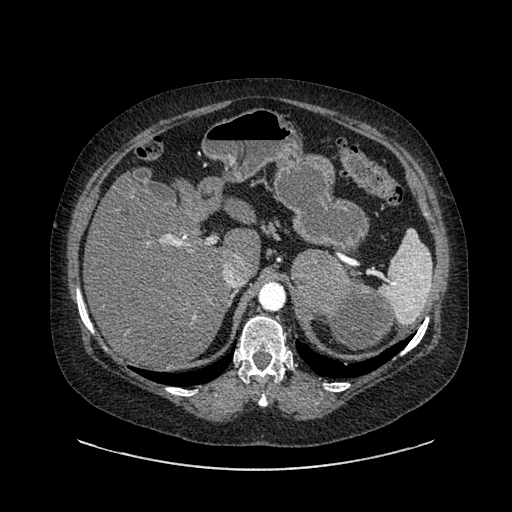
Contrast-enhanced abdominal CT, one axial slice; position 609 of 769 along the scan axis; reconstruction kernel SOFT; 120 kVp; soft-tissue window (W 400 / L 40 HU); 0.62 mm slice thickness; 512 × 512 image matrix, field of view 460 × 460 mm. Patient: female, 61 years. Case-level facts recorded for this patient, not image findings: diagnosis: adrenocortical carcinoma; tumour side: left adrenal; tumour size at pathology: 13 cm; Ki-67 index: 79 %; stage (as recorded): 2.
Annotated regions visible in this slice (semi-automatically segmented with operator editing):
- mass: bounding box <292,252,392,349> (left, top, right, bottom; pixels)